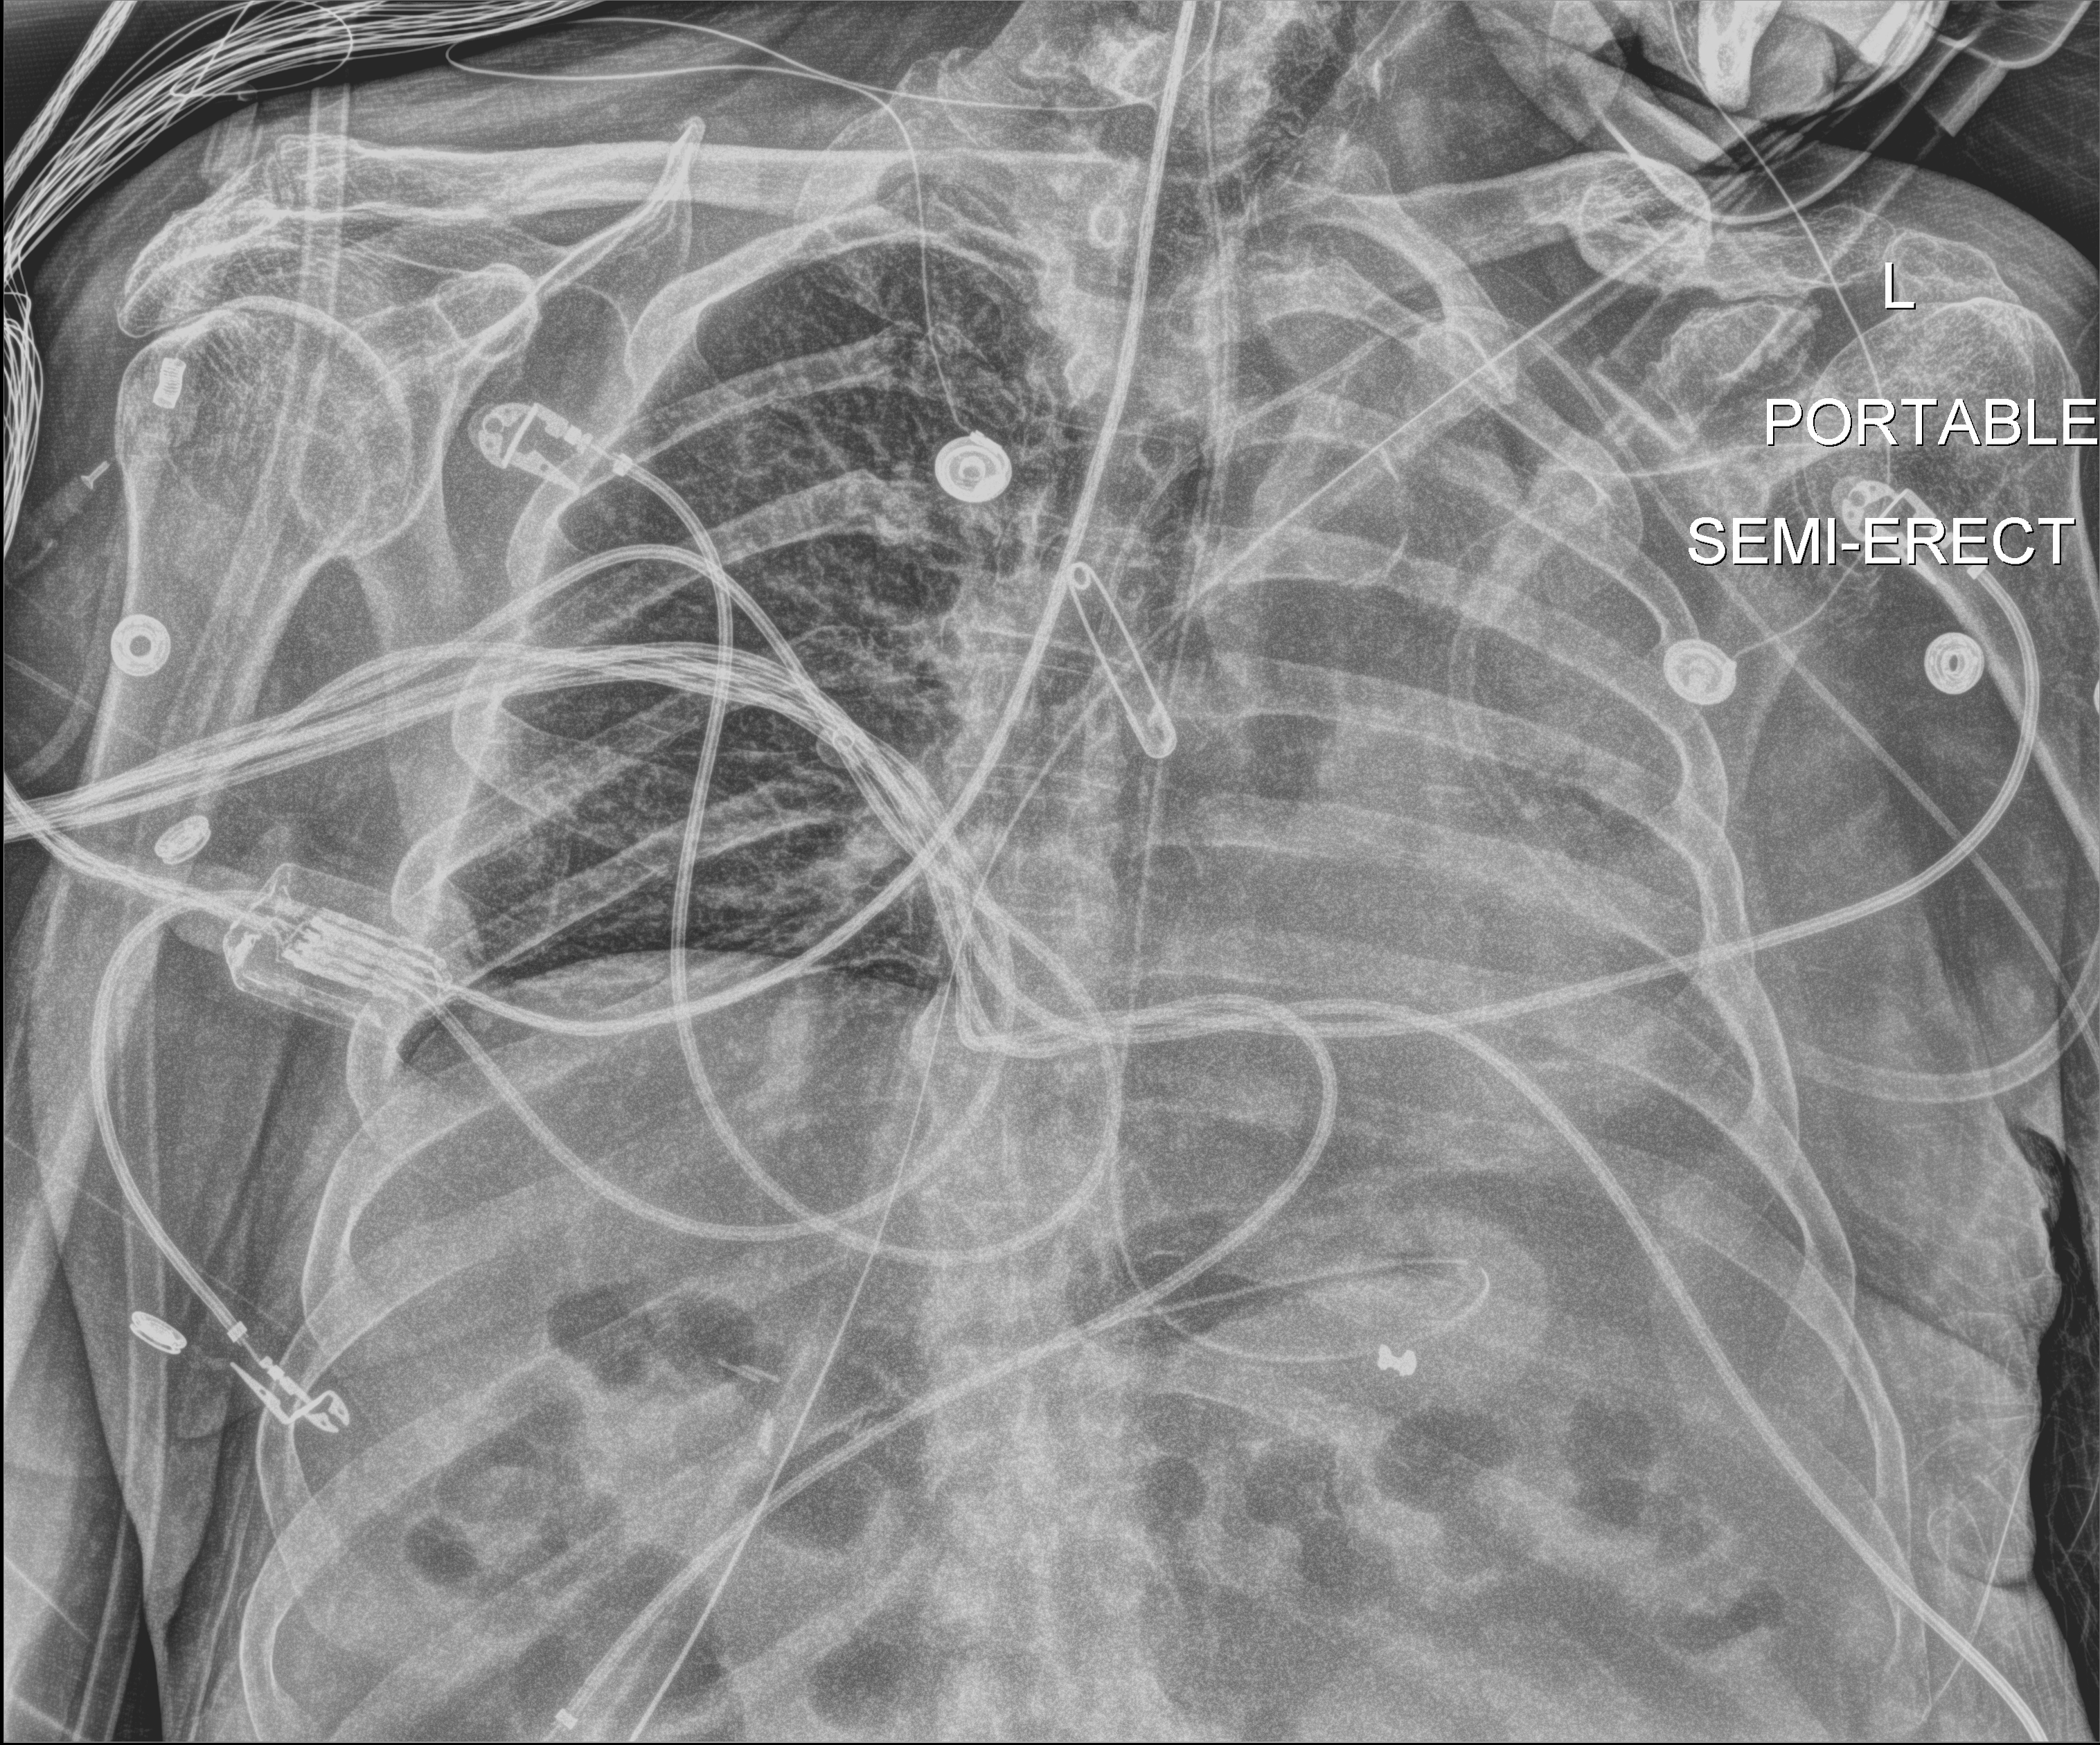
Bedside chest radiograph (digital radiography); anteroposterior (AP) projection. Patient hospitalised with COVID-19; male, aged 60–74 years.
From the hospital-stay record, not from the radiograph (when in the stay this image was taken is not recorded):
- admitted to intensive care during this hospital stay: no